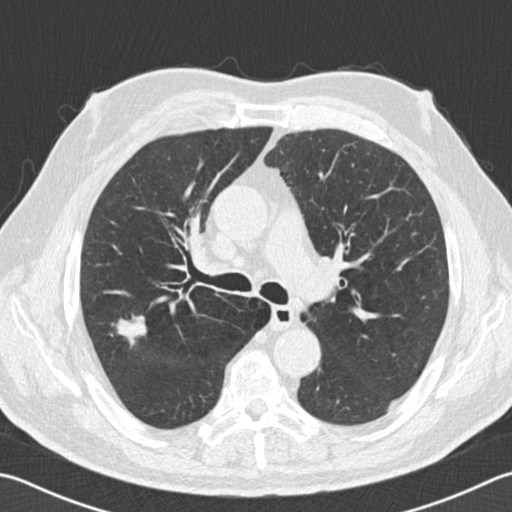
Low-dose screening chest CT, one axial slice; position 107 of 162 along the scan axis; lung window (W 1500 / L -600 HU); 2 mm slice thickness; 512 × 512 image matrix, field of view 346 × 346 mm.
Annotated regions visible in this slice (manually delineated by an expert):
- lesion 1 (tumor, upper lobe of right lung): bounding box [x1, y1, x2, y2] px = [117, 316, 146, 346]